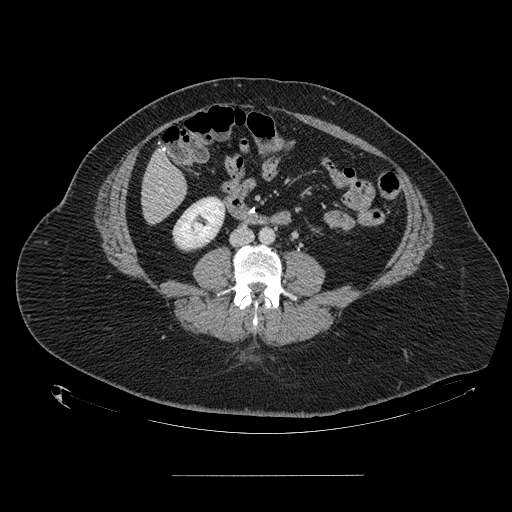
Contrast-enhanced abdominal CT, one axial slice; position 25 of 164 along the scan axis; 120 kVp; intravenous contrast given; soft-tissue window (W 400 / L 40 HU); 2.5 mm slice thickness; 512 × 512 image matrix. Female patient, age 52 years. From the clinical record (not read from this slice): diagnosis: colorectal cancer liver metastases, imaged before liver resection; multiple liver metastases: yes; largest metastasis: 3.5 cm; disease in both lobes: no.
Structures marked on this image (manually delineated by an expert):
- hepatic veins: box from (x=160, y=188) to (x=163, y=191) px
- liver: (x=143, y=153)–(x=186, y=223)